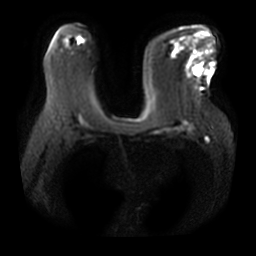
Breast MRI, one axial slice; diffusion-weighted series; image 2 of 4 stored at this slice position (different b-values; order by instance number); 3 T; 5 mm slice thickness; 256 × 256 image matrix, field of view 380 × 380 mm. Female patient.
Structures marked on this image (outlined manually by an expert reader):
- tumour on diffusion-weighted imaging: bounding box (x1, y1, x2, y2) in pixels: (194, 66, 200, 75)